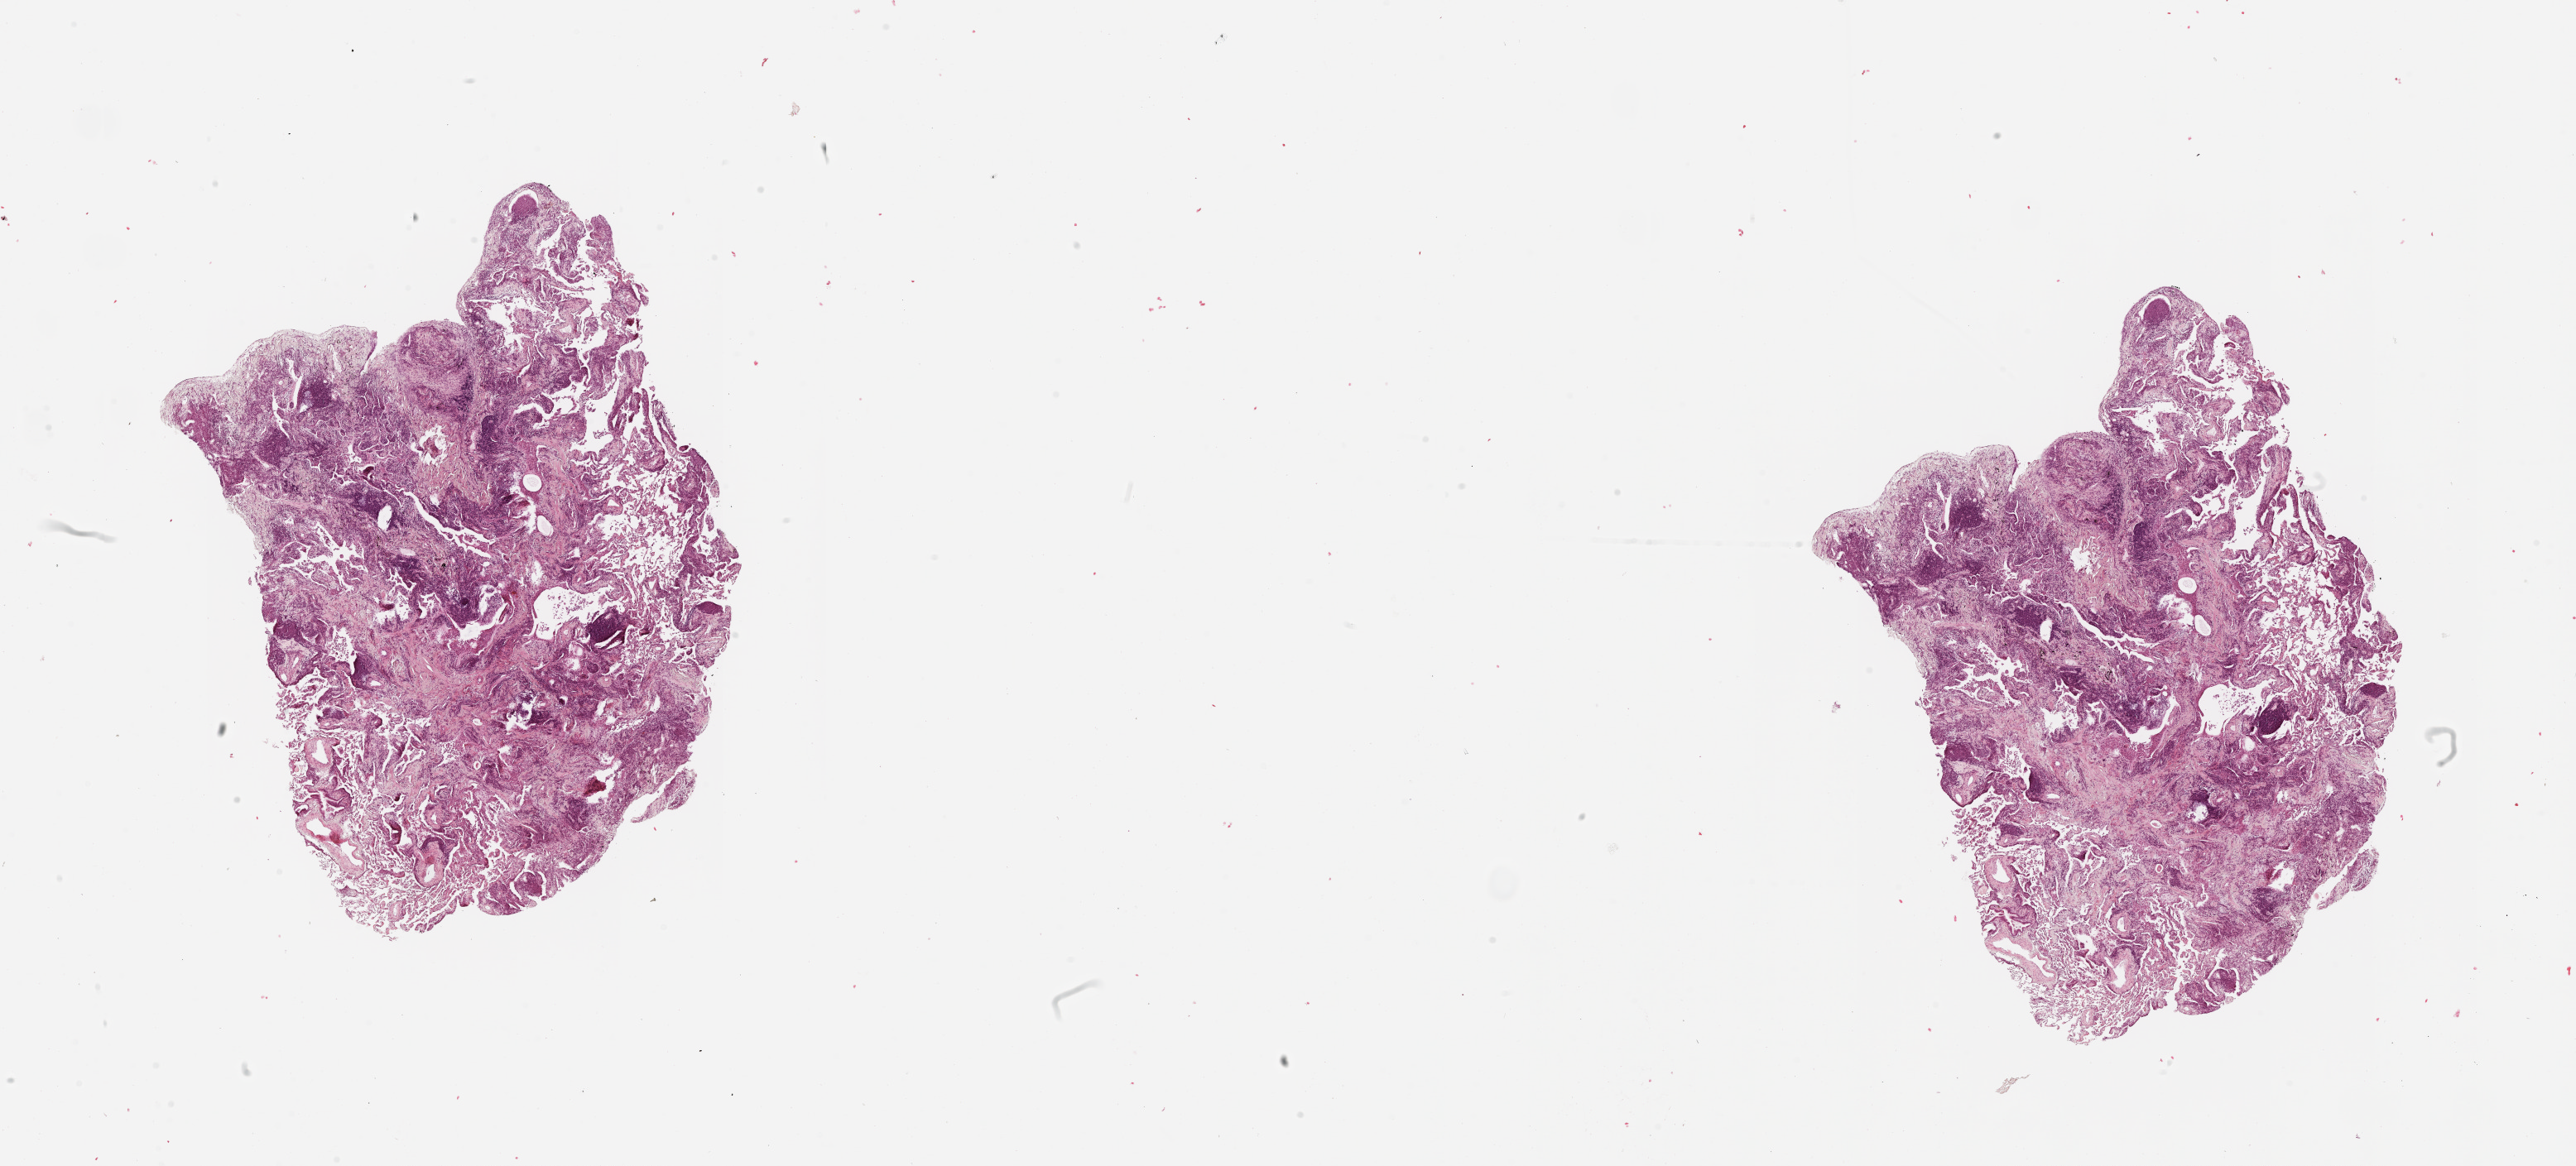
H&E-stained whole-slide image, whole scanned area (about 25.1 x 11.3 mm, acquisition: 20x scan) shown as a low-resolution overview; lung, tissue type not recorded.
Patient diagnosis (cohort enrolment): squamous cell carcinoma (lung).